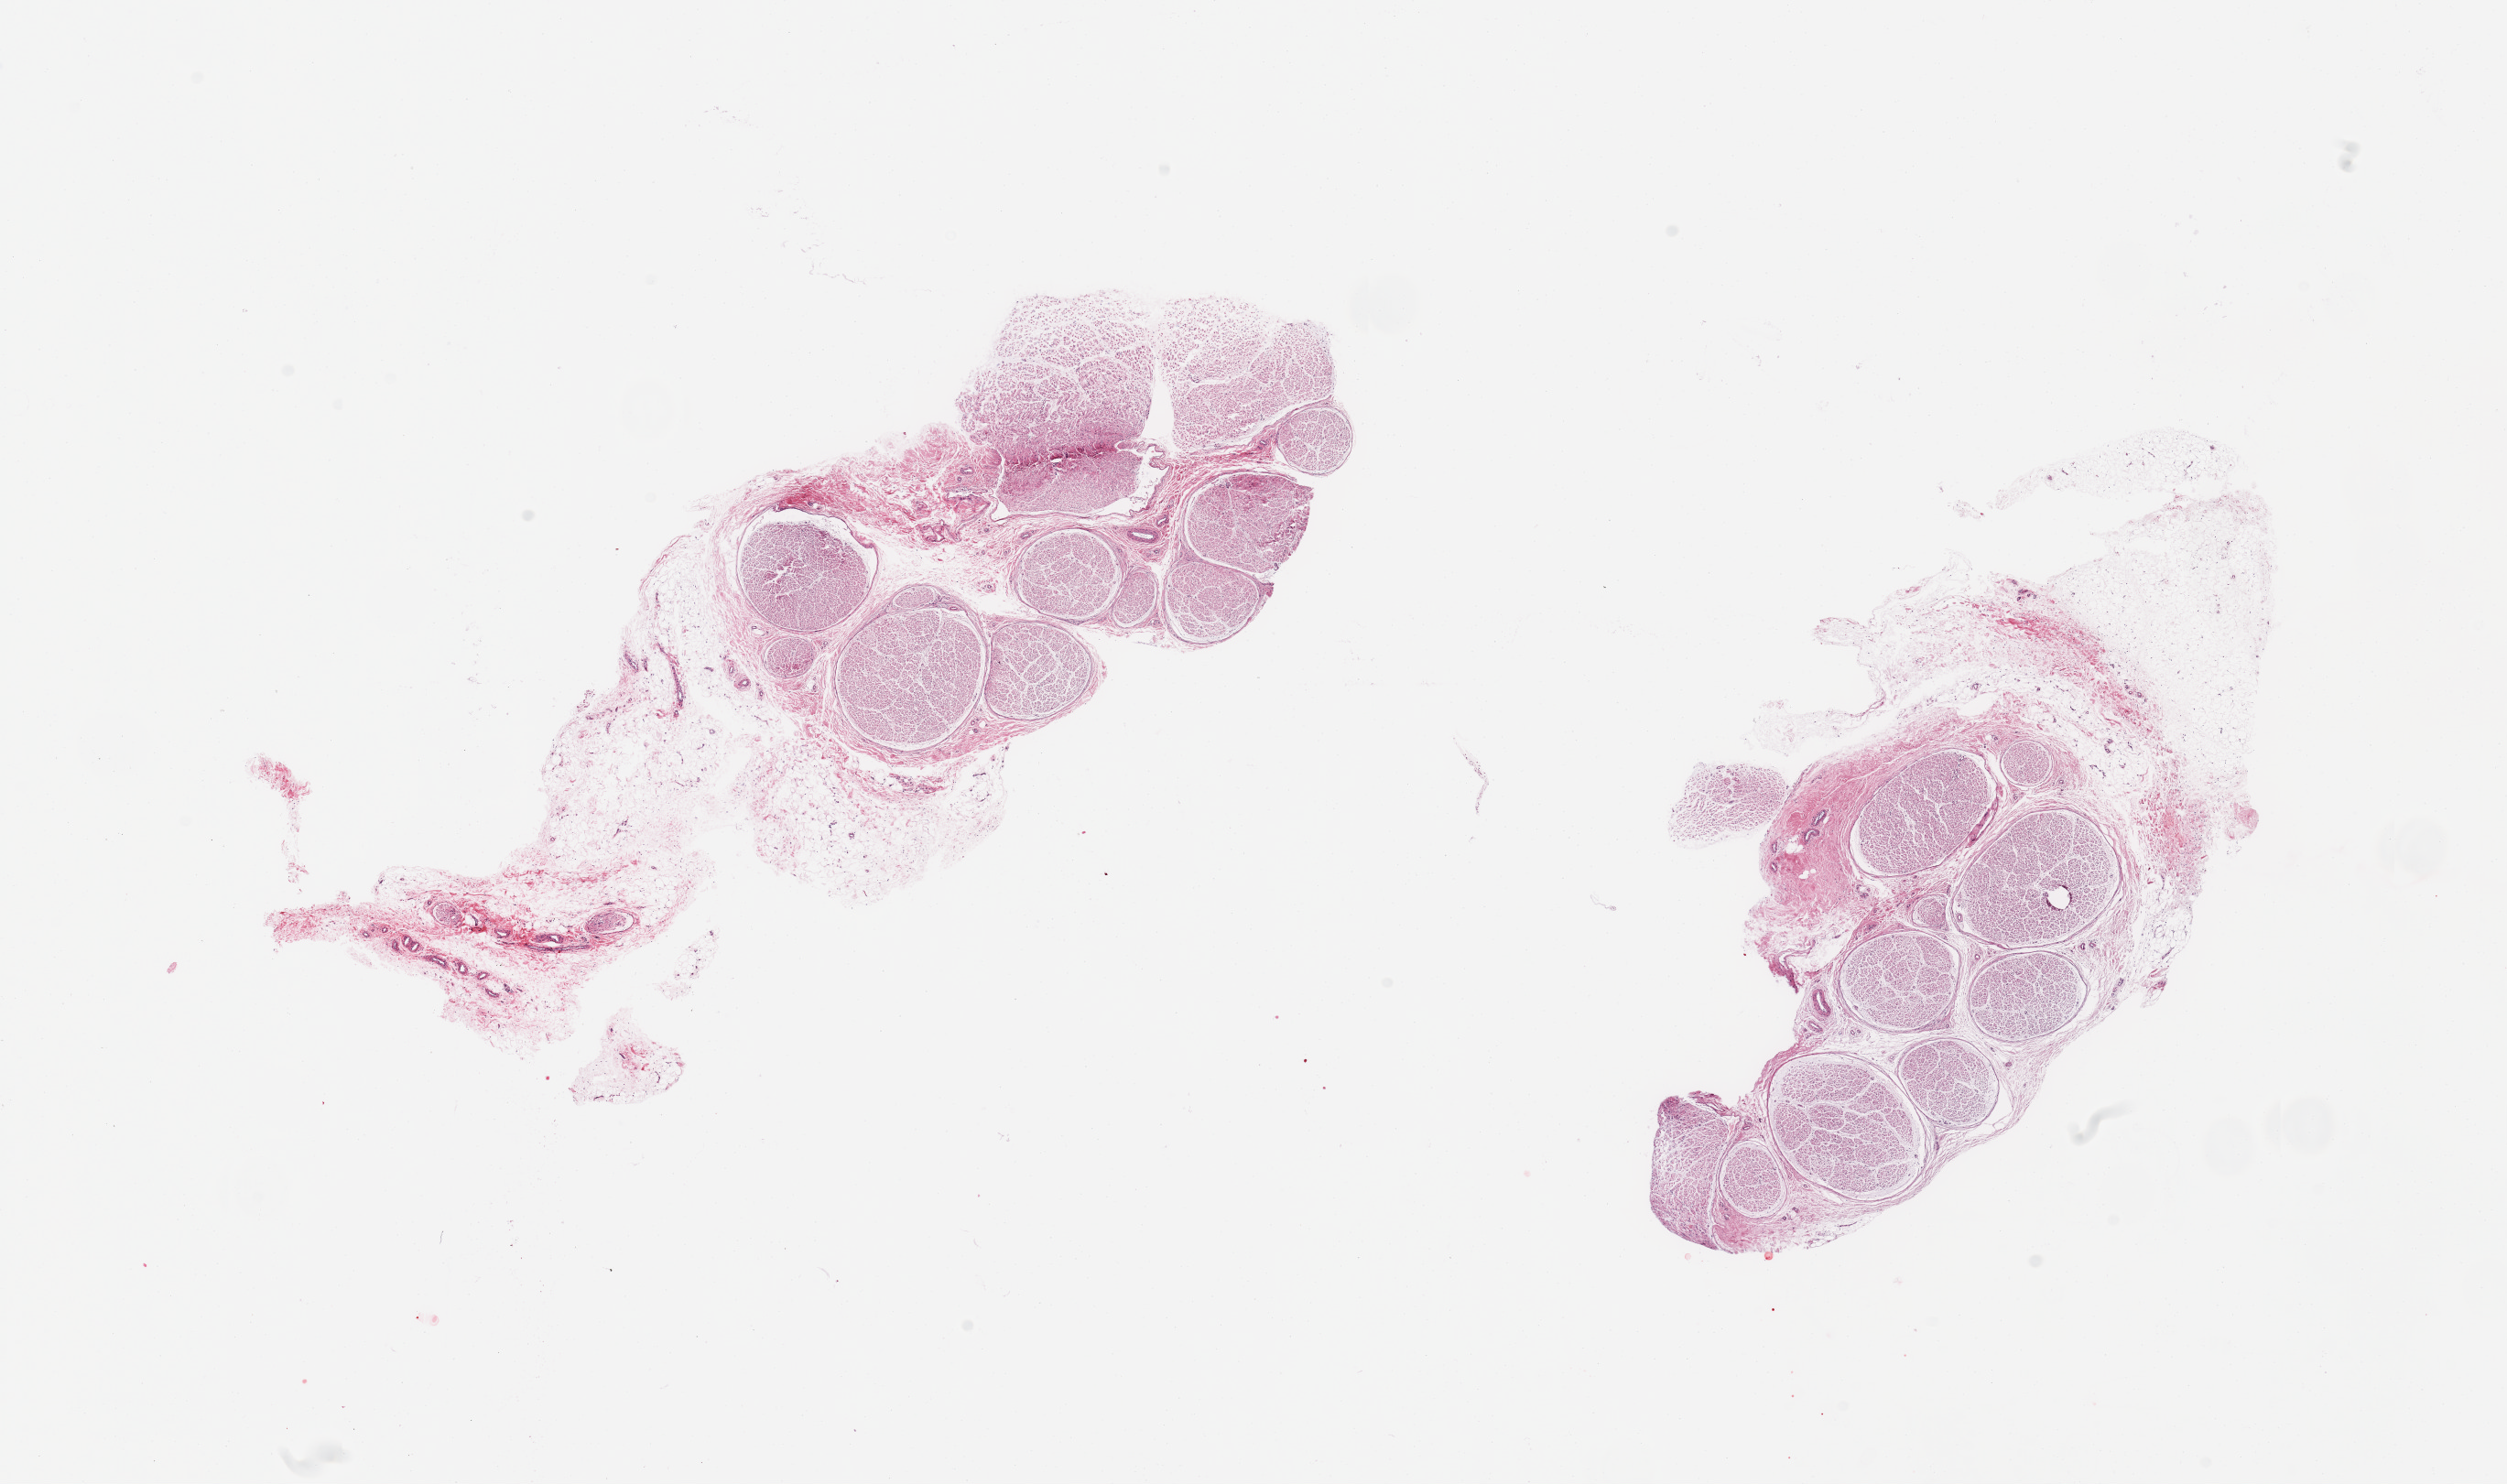
H&E whole-slide image, a low-resolution overview of the entire scanned area, about 21.7 x 12.8 mm (from a 20x scan), PAXgene-fixed paraffin-embedded (PFPE) section, sampled site (target tissue): tibial nerve, tissue donor sample.
Reviewer comment on this tissue sample: 2 pieces; both include from 30-40% attached fat.